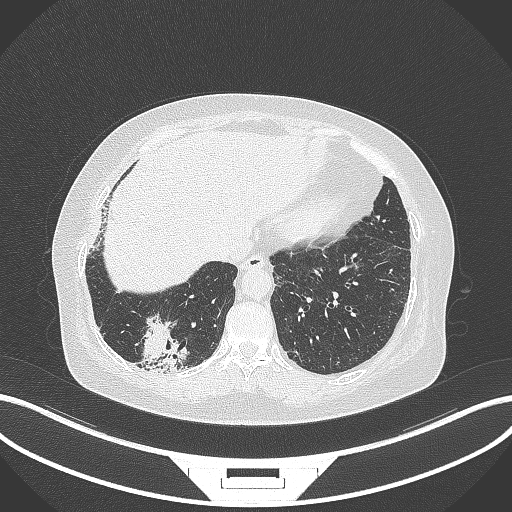
Chest CT, one axial slice; slice 38 of 296 in the series (ordered by position); 120 kVp; lung window (W 1500 / L -600 HU); 1 mm slice thickness; 512 × 512 image matrix, field of view 400 × 400 mm. Female patient, age 65 years. Case-level facts recorded for this patient, not image findings: clinical TNM (as recorded): T2b N1 M0.
Structures marked on this image (bounding box drawn by a radiologist):
- lung tumour (recorded histology: adenocarcinoma): bounding box <135,313,191,374> (left, top, right, bottom; pixels)